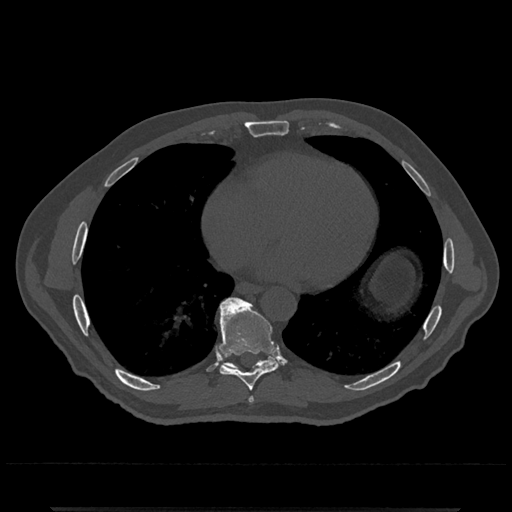
CT including the spine, one axial slice; slice 654 of 797 in the series (ordered by position); reconstruction kernel Br40s/3; 120 kVp; bone window (W 1800 / L 400 HU); 512 × 512 image matrix, field of view 393 × 393 mm. Patient: male, 67 years. Case-level facts recorded for this patient, not image findings: primary cancer: prostate.
Annotated regions visible in this slice (semi-automatically segmented with operator editing):
- T7 vertebra: bounding box (x1, y1, x2, y2) in pixels: (249, 397, 254, 402)
- T8 vertebra: (219, 297, 280, 391)
- T9 vertebra: (218, 298, 278, 370)